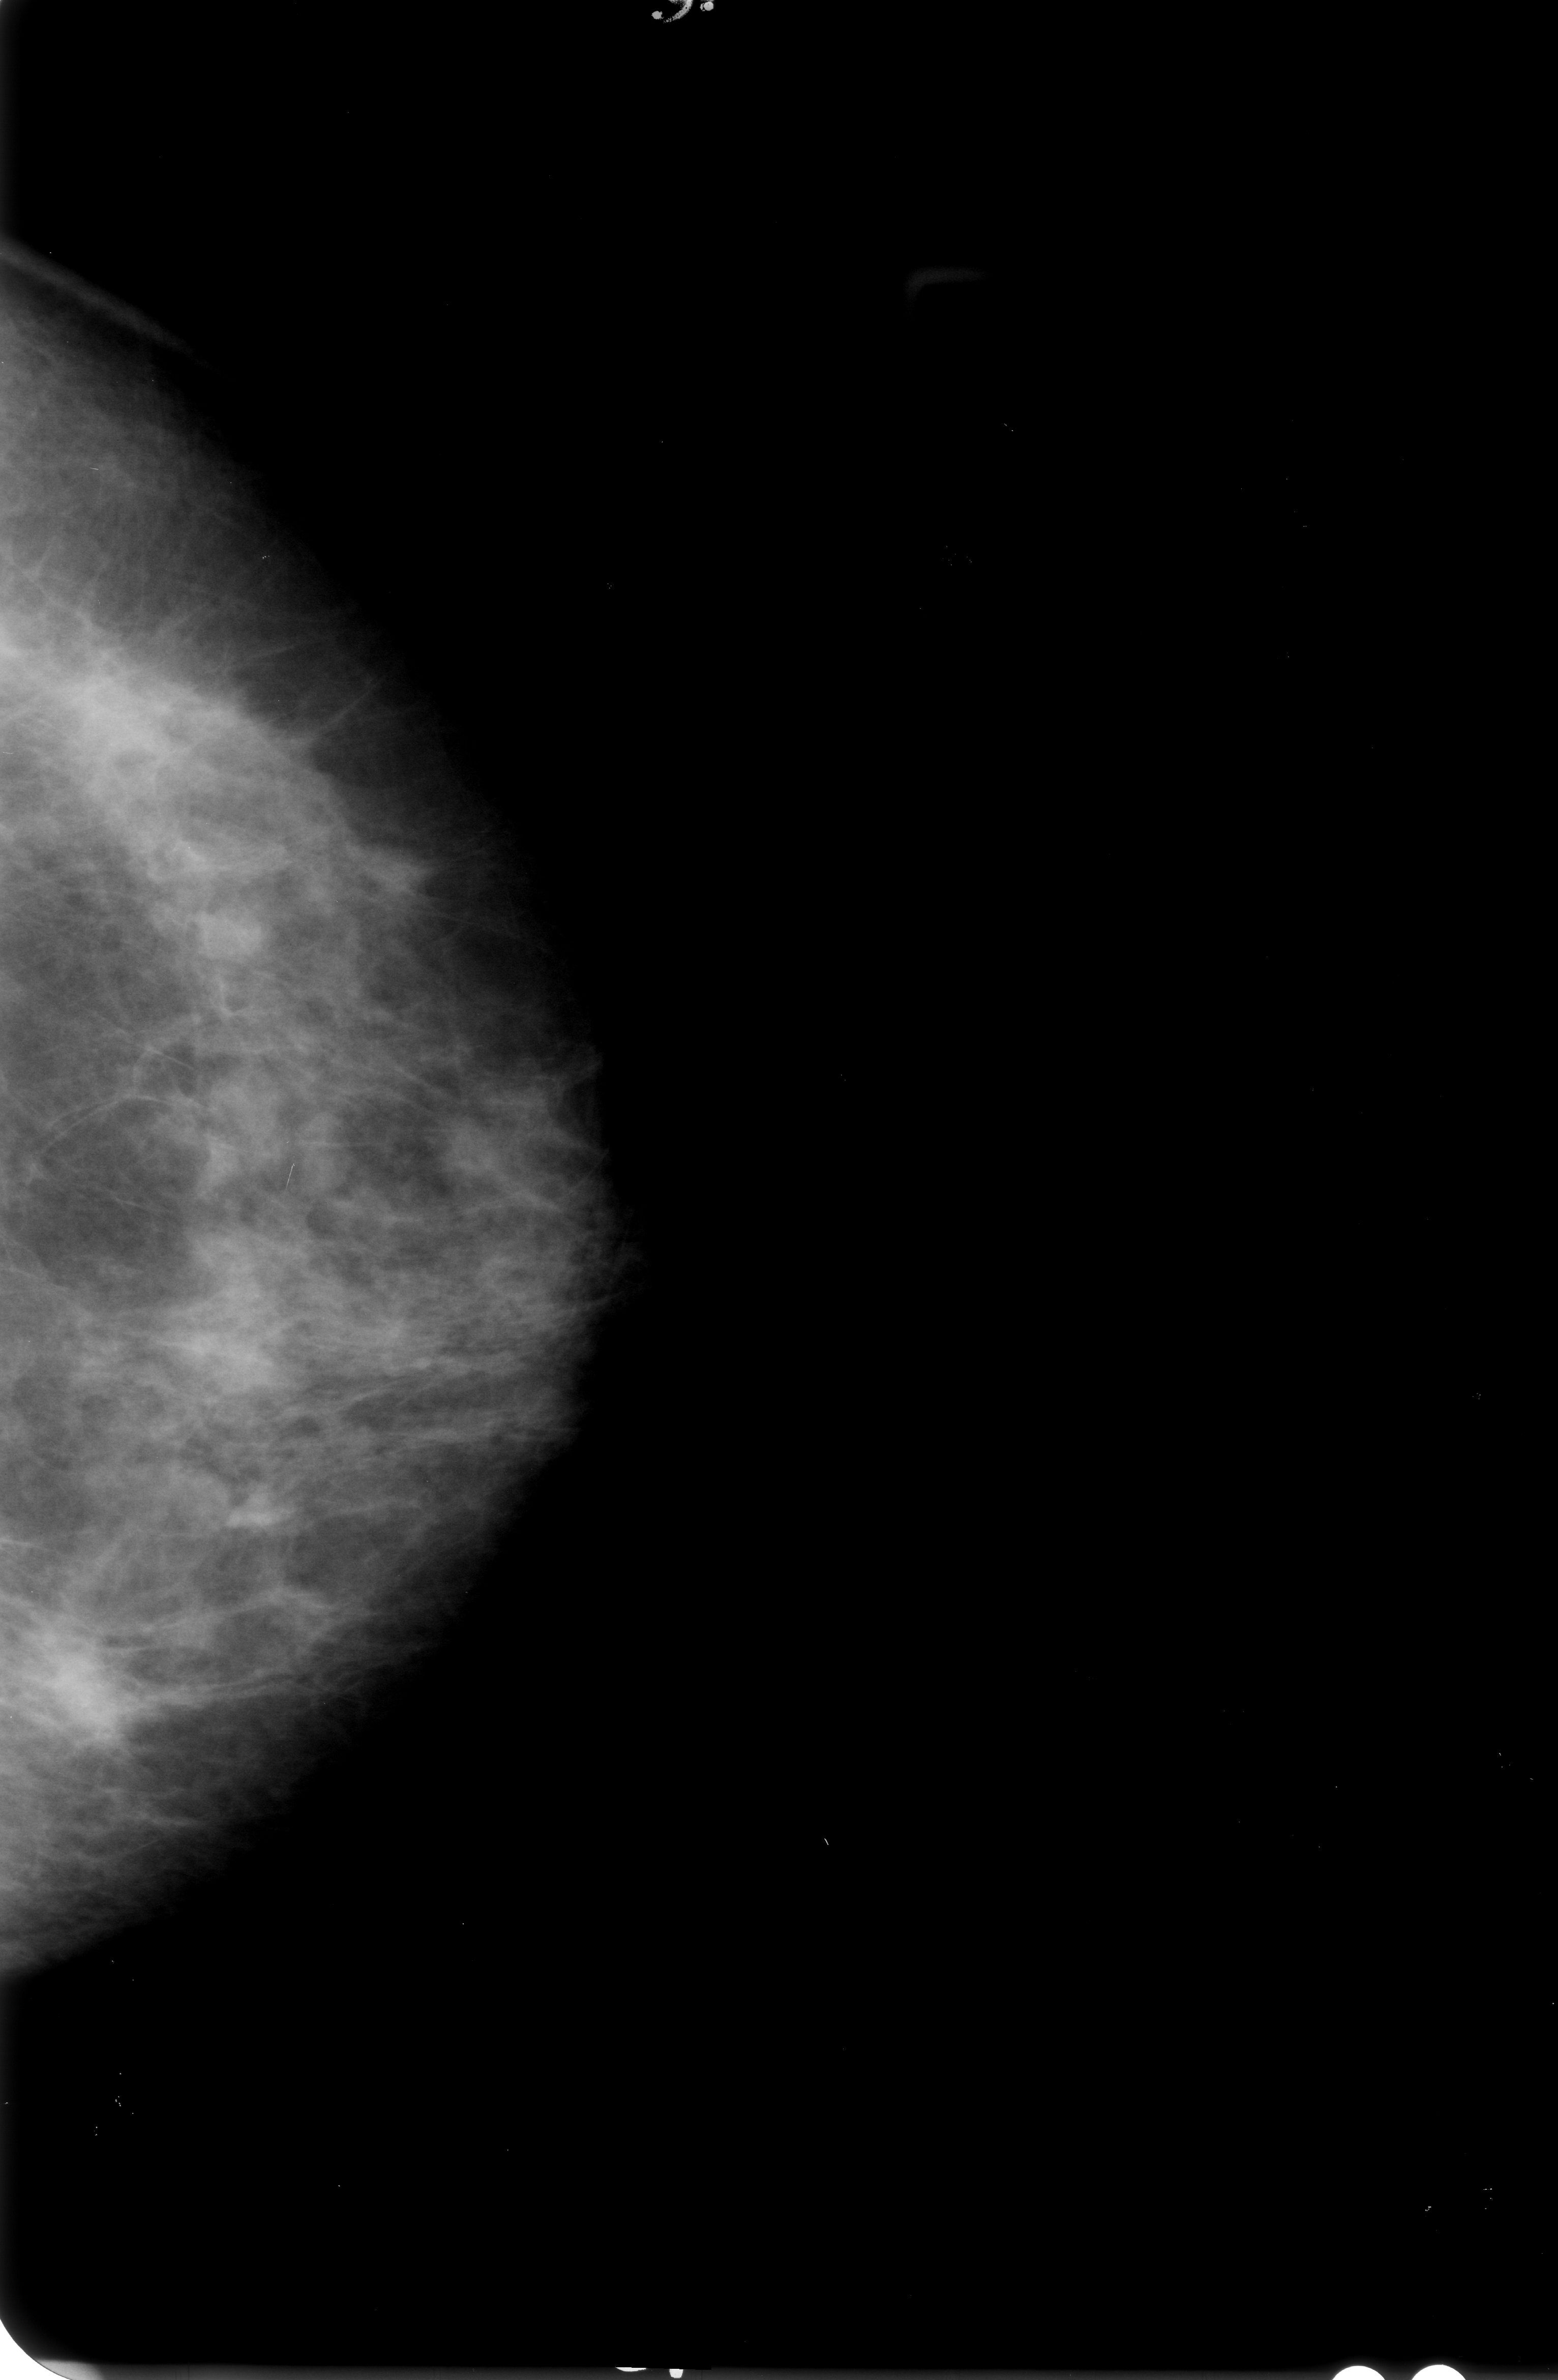
Scanned film-screen mammogram; left breast; CC view; BI-RADS breast density category 3 (scale 1–4).
Abnormality record for this image: calcifications, morphology pleomorphic, distribution clustered; BI-RADS assessment category 4; subtlety rating 3 on a 1 (subtle) to 5 (obvious) scale; pathology result (as recorded, not read from the image): malignant.